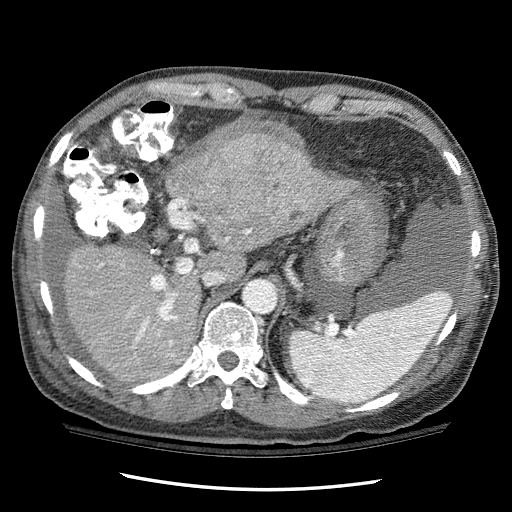
Contrast-enhanced abdominal CT (liver protocol), one axial slice. Reconstruction kernel STANDARD. 120 kVp. One of 3 acquisitions stored at this slice position. Soft-tissue window (W 400 / L 40 HU). 2.5 mm slice thickness. 512 × 512 image matrix, field of view 360 × 360 mm. From the clinical record (not read from this slice): diagnosis: hepatocellular carcinoma (patient treated with transarterial chemoembolisation; whether this scan precedes or follows treatment is not stated here); TNM stage (as recorded): Stage-I; Child-Pugh class: C.
Outlined on this slice (semi-automatic segmentation, software-assisted and operator-edited):
- liver parenchyma outside the tumour (the mass and vessels are separate outlines, so this box may not span the whole liver): bounding box <64,138,358,382> (left, top, right, bottom; pixels)
- mass: <164,132,316,226>
- liver vessels: <99,229,251,357>